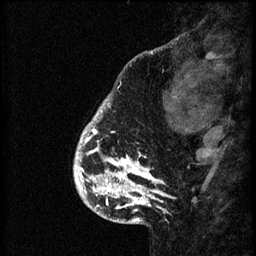
Breast MRI (dynamic contrast-enhanced), one sagittal slice. Slice 13 of 60 in the series (ordered by position). 3 images stored at this slice position (order not interpretable as contrast timing). 1.5 T. TE 4.2 ms, TR 8.2 ms. 2 mm slice thickness. 256 × 256 image matrix, field of view 180 × 180 mm. Patient: female, 41 years.
Annotated regions visible in this slice (semi-automatic segmentation, software-assisted and operator-edited):
- analysis volume of interest (the breast-tissue region the enhancement analysis was run in; not a lesion): bounding box <75,108,176,205> (left, top, right, bottom; pixels)
- tumour enhancement mask (voxels above the 70 % enhancement threshold inside the analysis volume of interest): <75,108,167,205>